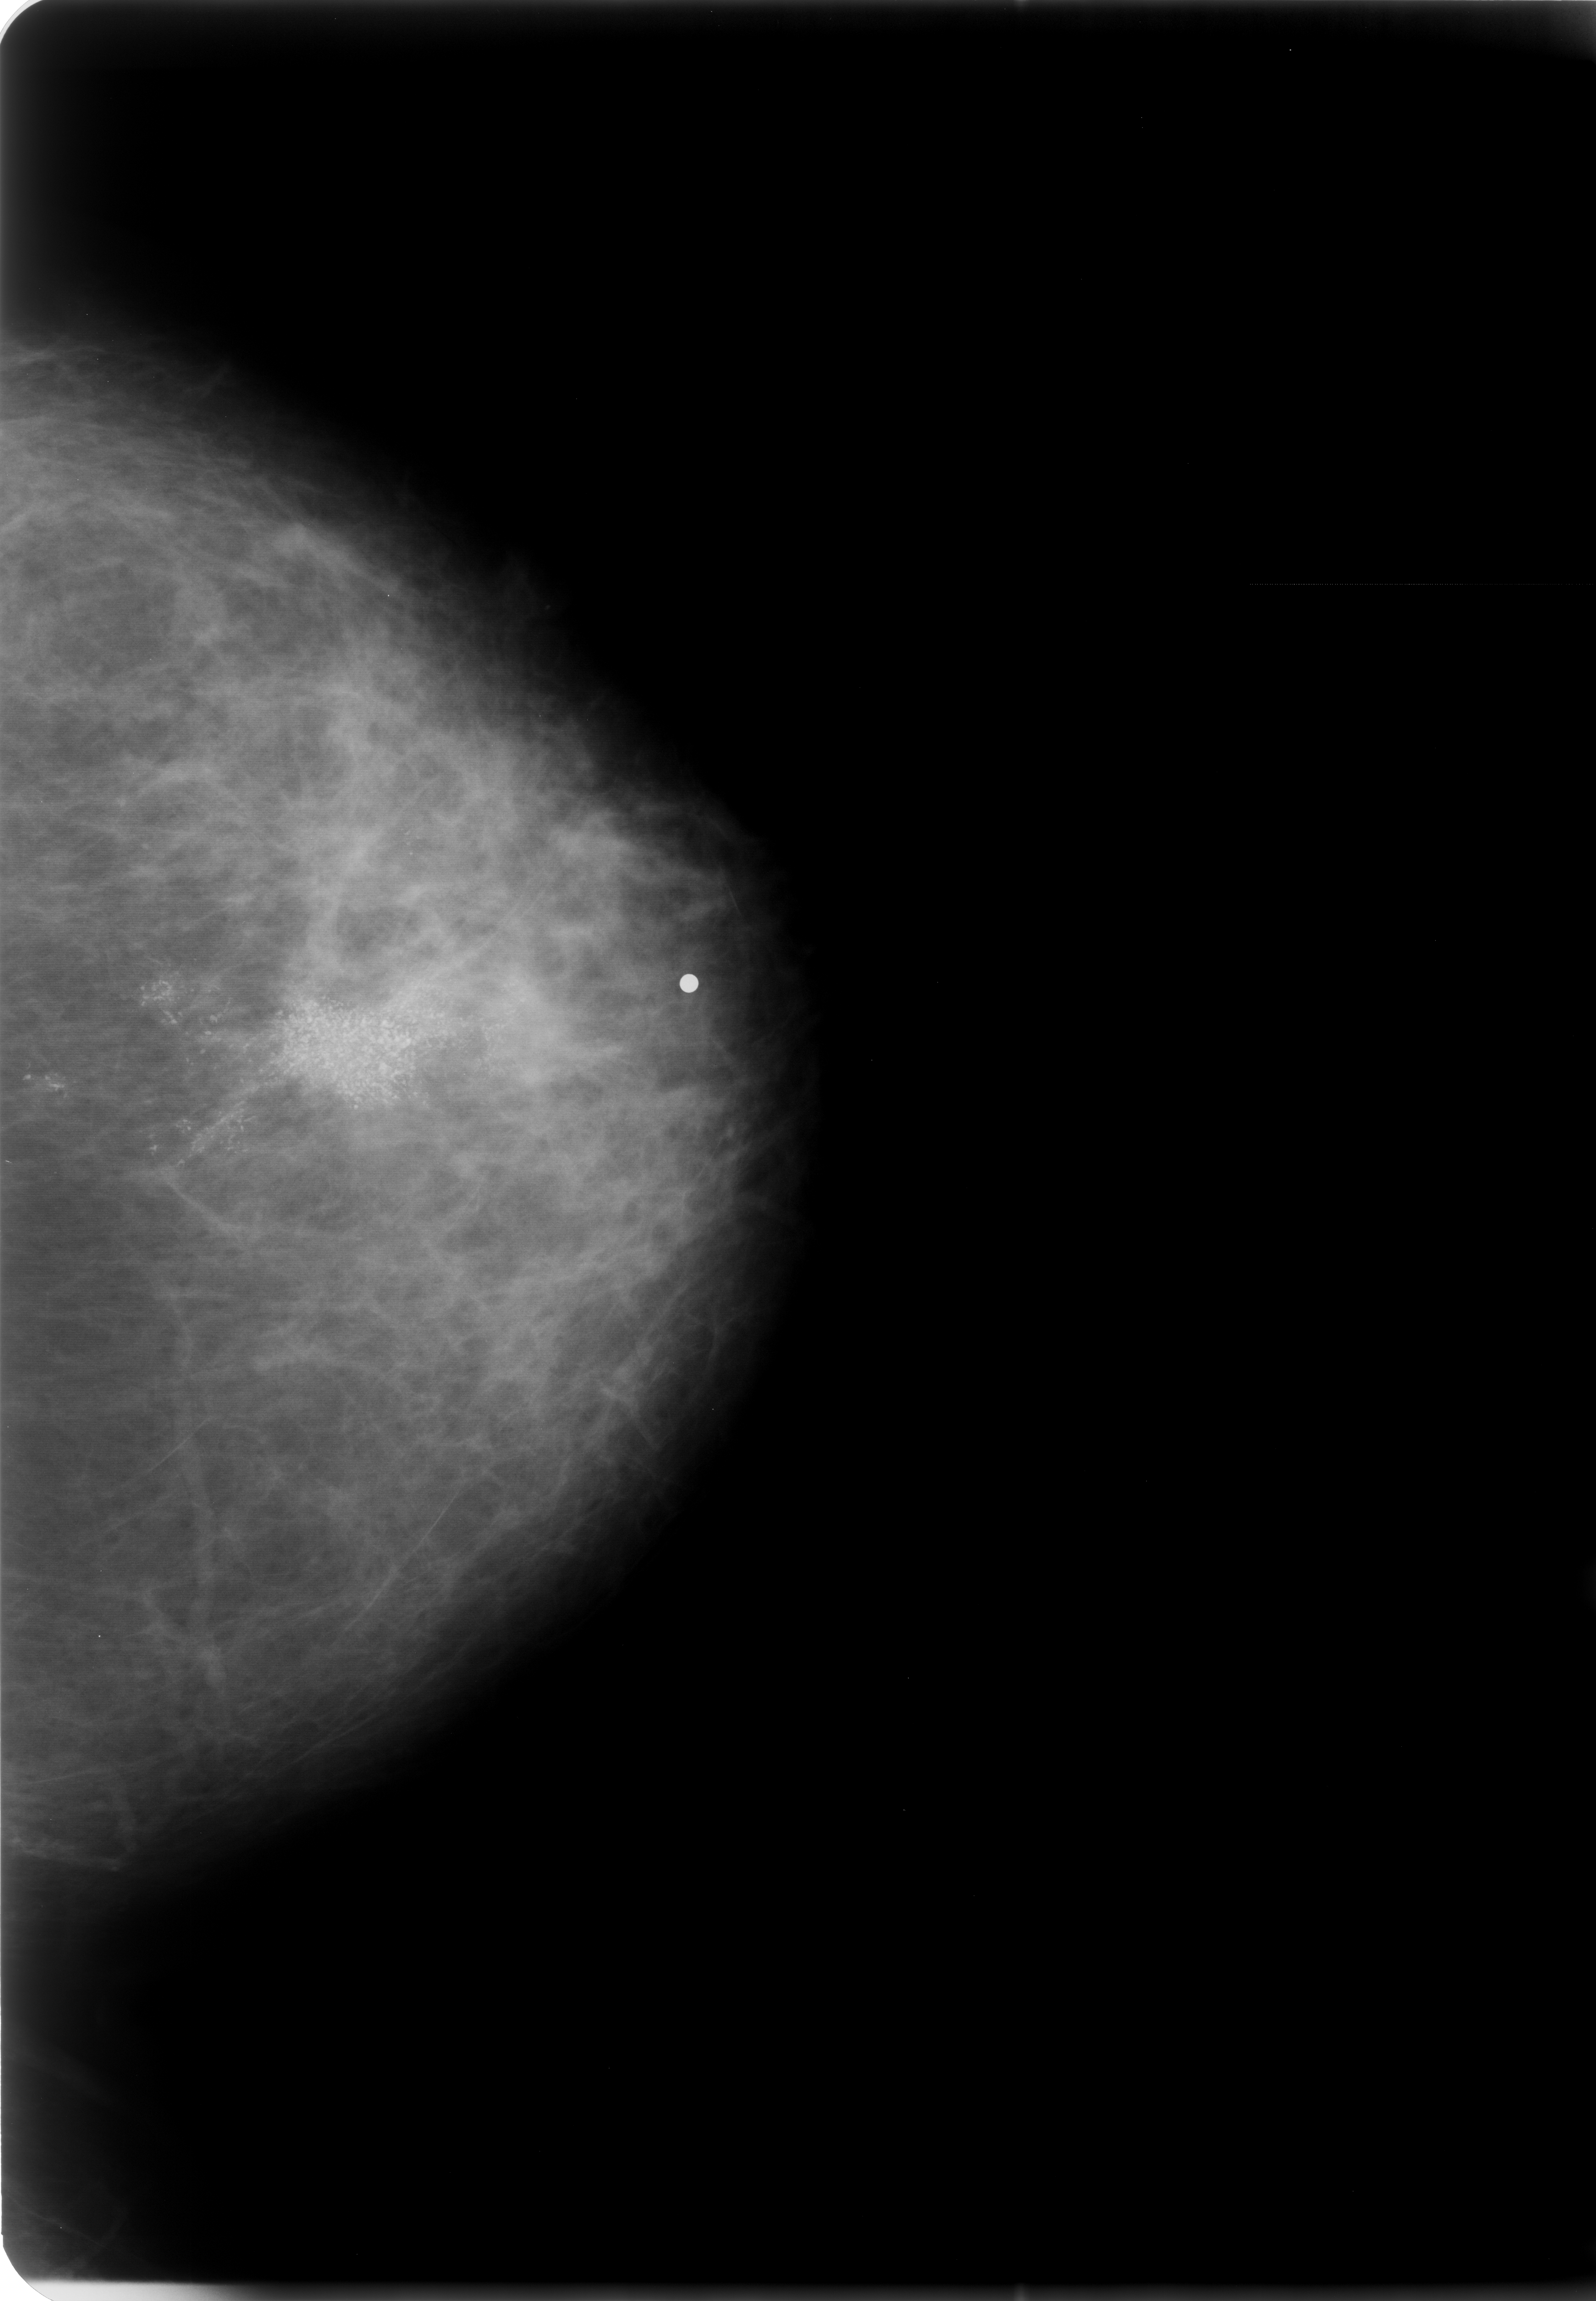
Scanned film-screen mammogram, left breast, CC view, BI-RADS breast density category 2 (scale 1–4).
Calcifications, morphology pleomorphic, distribution segmental; BI-RADS assessment category 5; pathology result (as recorded, not read from the image): malignant.